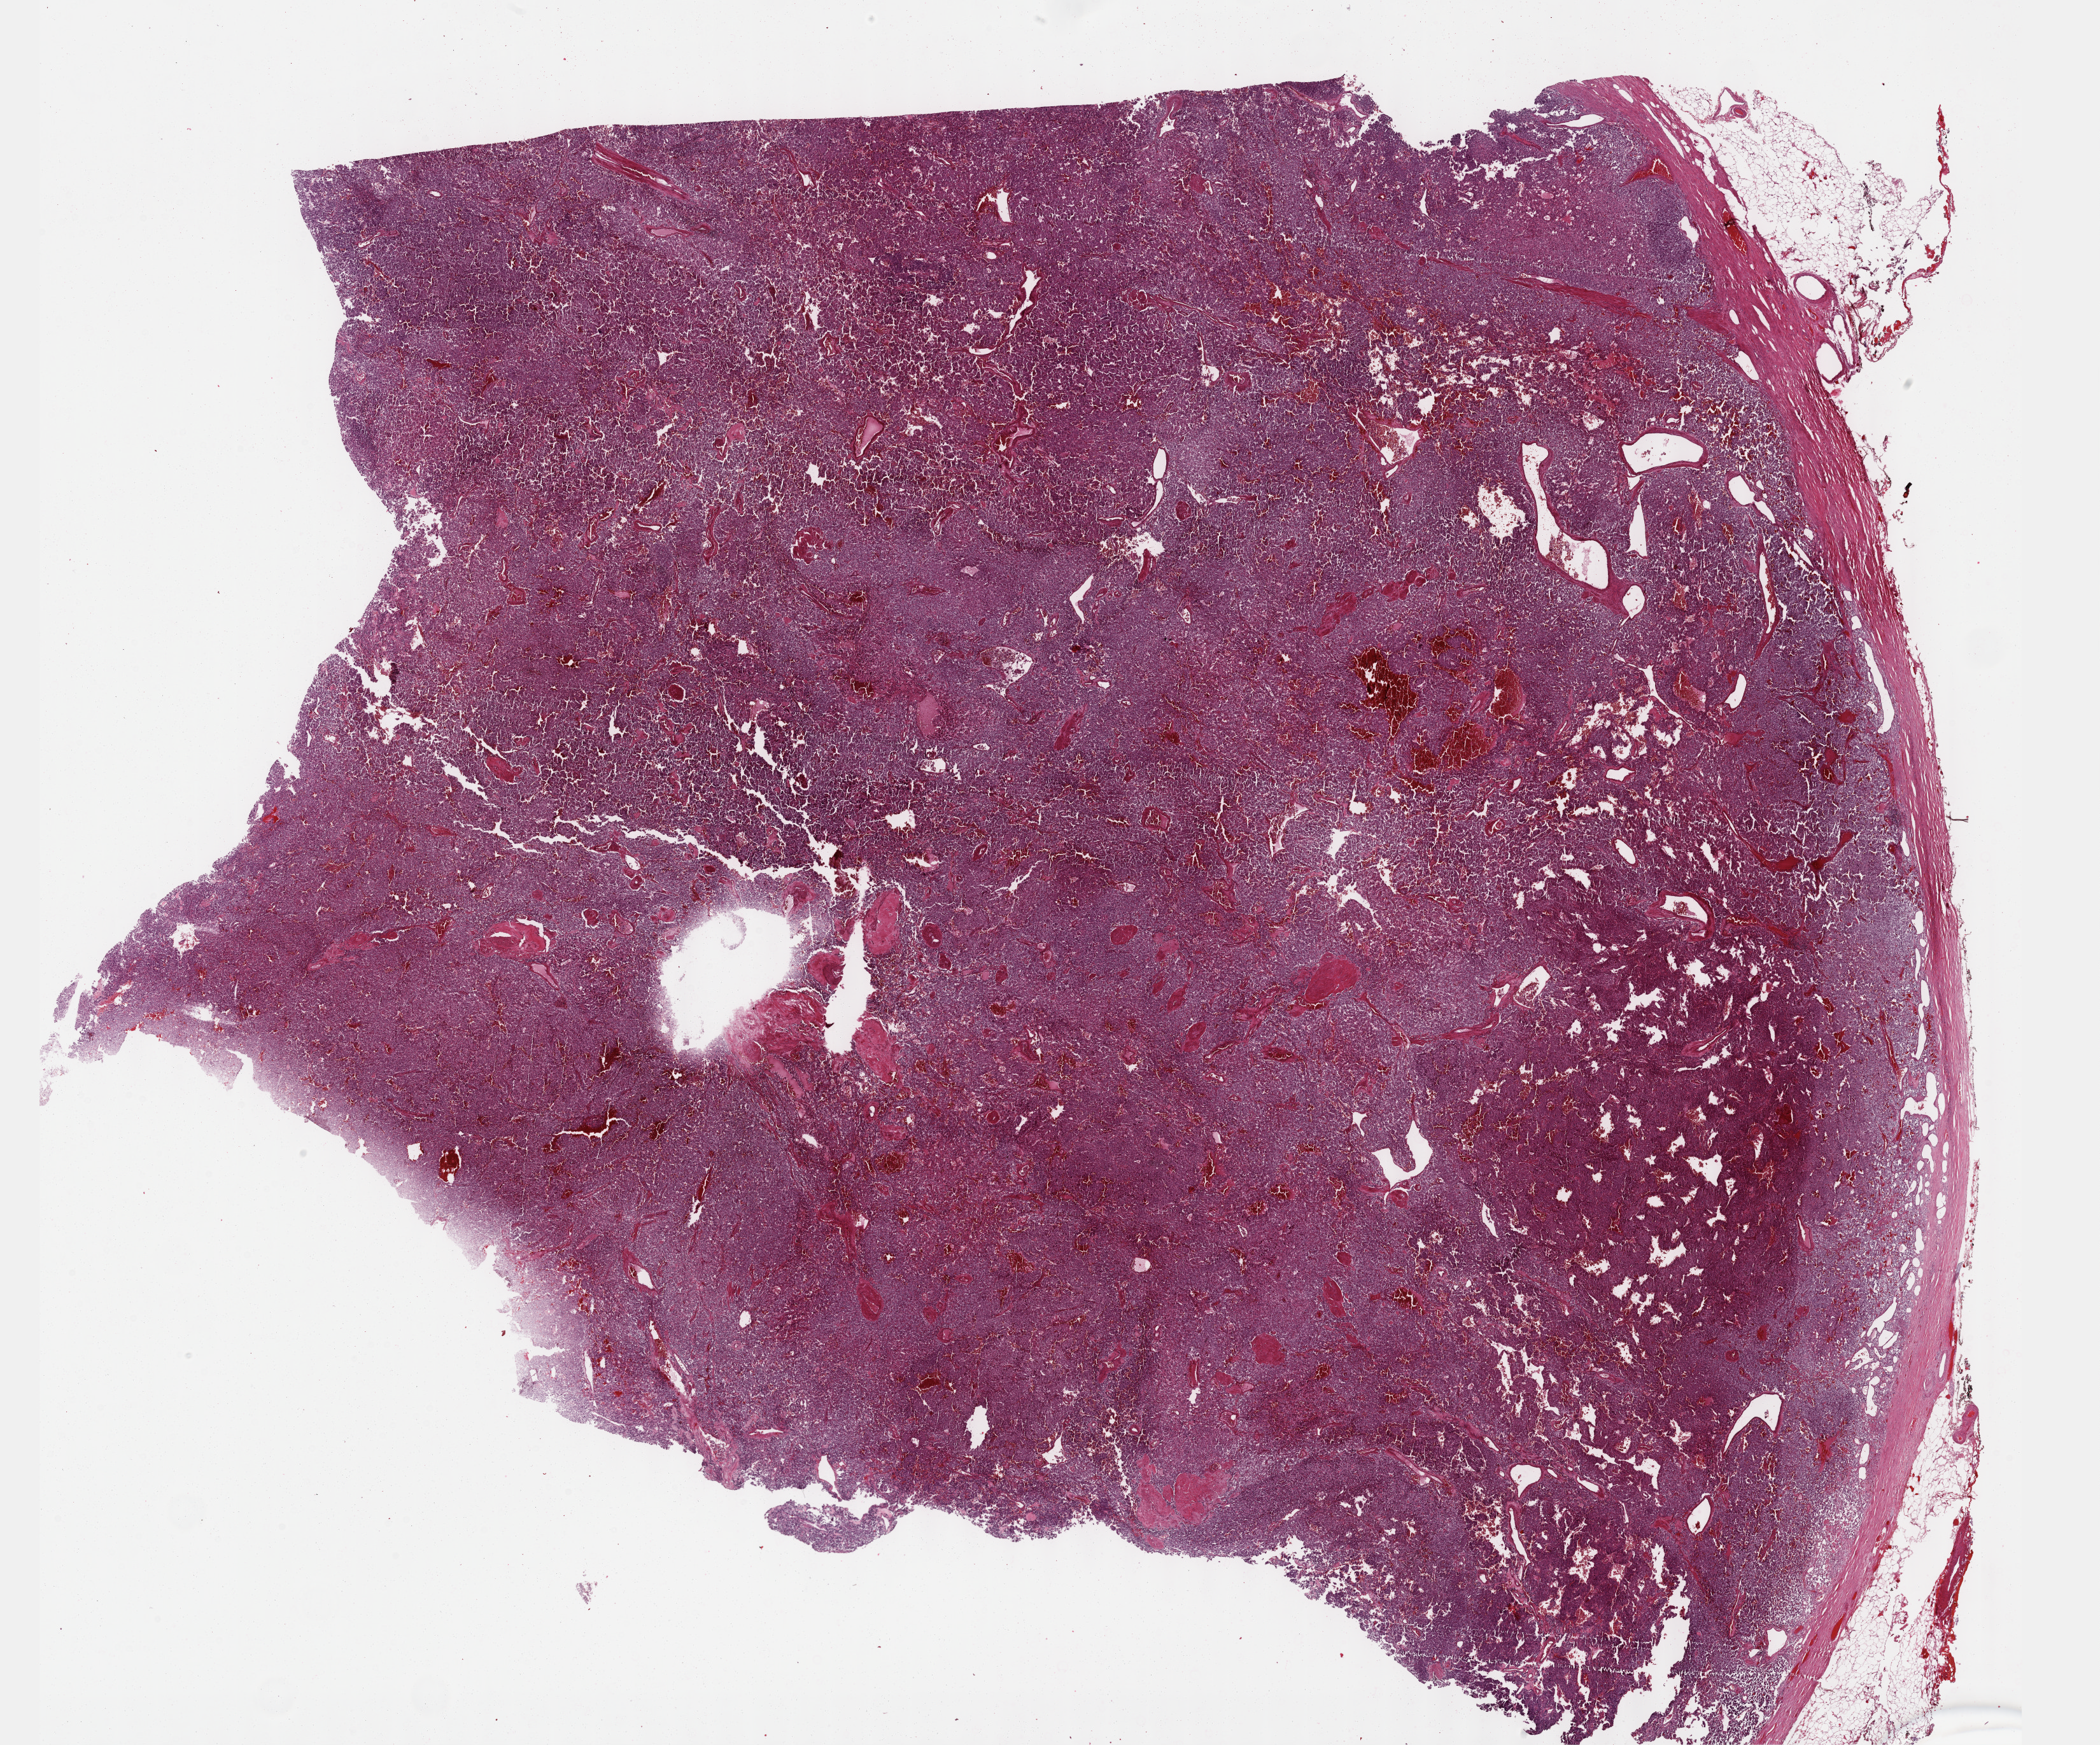
Whole-slide histology image, H&E-stained, shown as a low-resolution overview of the whole scanned area (about 26.7 x 22.2 mm). Formalin-fixed paraffin-embedded (FFPE) diagnostic section. Primary tumour sample from the adrenal gland. Patient: male, age at initial diagnosis 63 years.
- histologic diagnosis: Pheochromocytoma, NOS